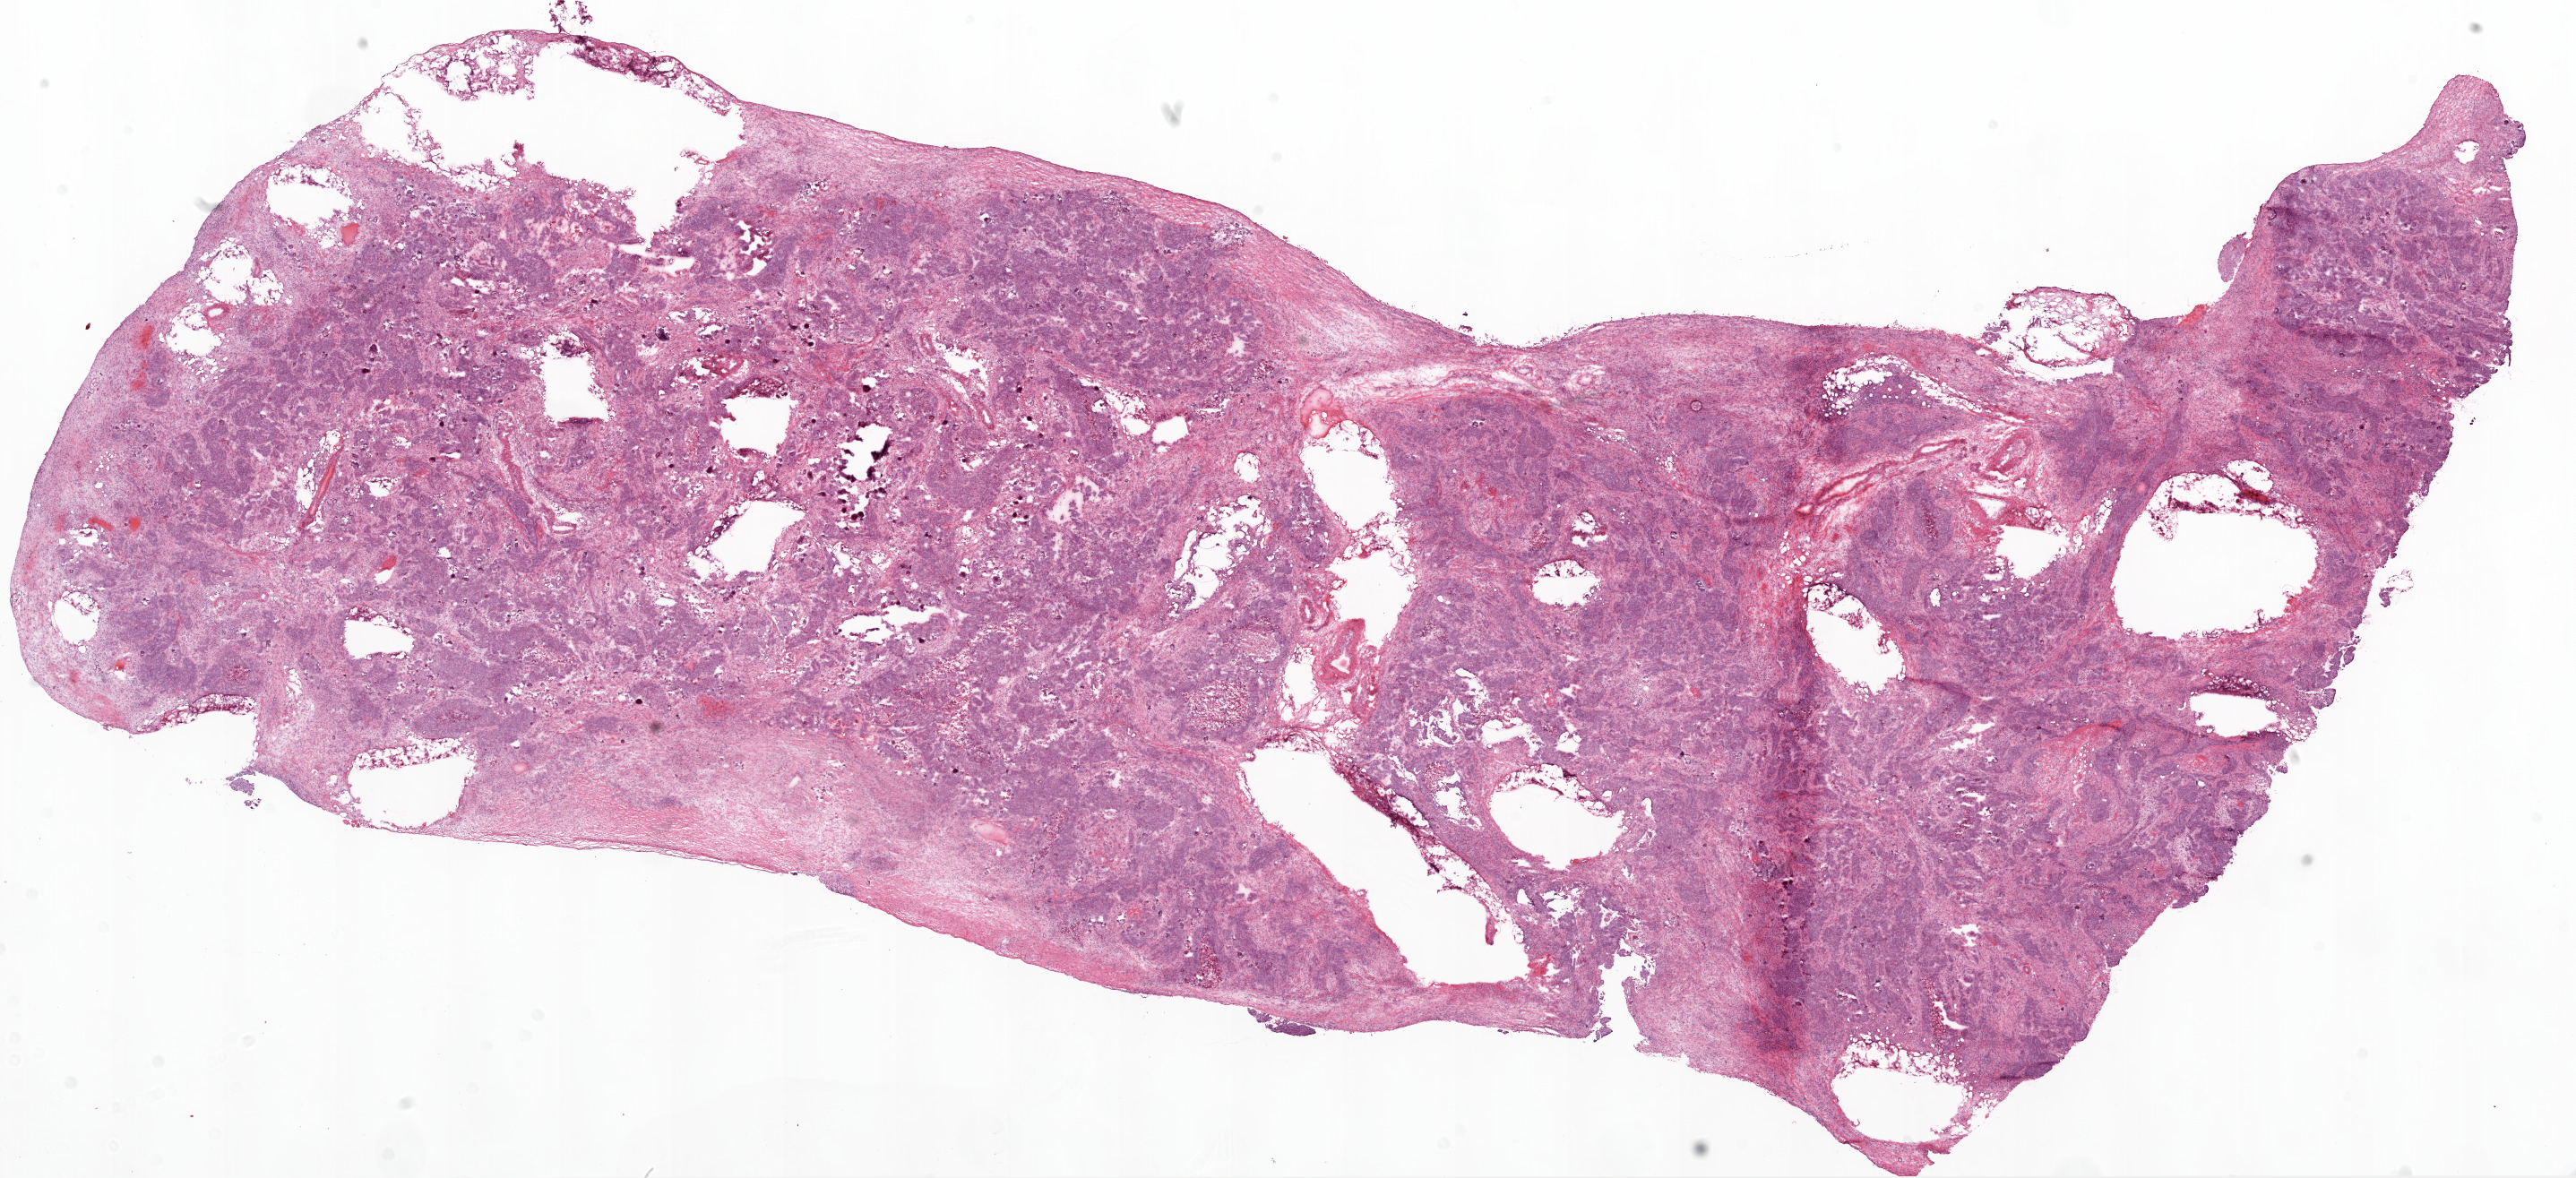
Whole-slide histology image, H&E, shown as a low-resolution overview of the whole scanned area (about 23.1 x 10.6 mm). Frozen section. Primary tumour sample from the ovary. Patient: female, age at initial diagnosis 67 years. Histologic grade: G3 (poorly differentiated). Composition of this section per pathologist review: tumour cells 85%, tumour nuclei 95%, normal cells 0%, stromal cells 10%, necrosis 5%.
Pathologic diagnosis: Serous cystadenocarcinoma, NOS. FIGO stage: IIIC.